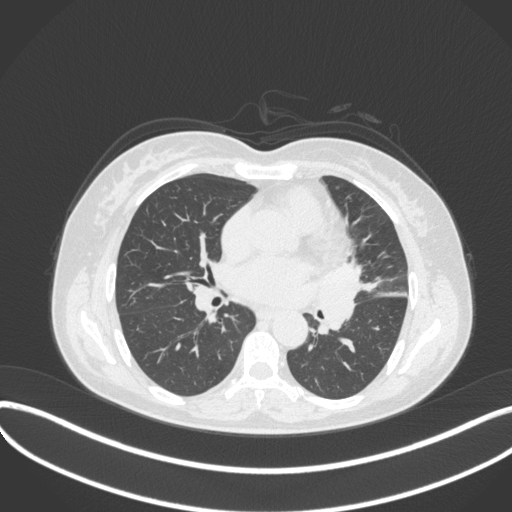
Chest CT, one axial slice. Slice 178 of 373 in the series (ordered by position). Reconstruction kernel B31f. Lung window (W 1500 / L -600 HU). 1 mm slice thickness. 512 × 512 image matrix, field of view 400 × 400 mm. Female patient, age 54 years. Case-level facts recorded for this patient, not image findings: clinical TNM (as recorded): T2a N1 M0; histopathological grade: G3.
Outlined on this slice (bounding box drawn by a radiologist):
- lung tumour (recorded histology: small cell carcinoma): bounding box (x1, y1, x2, y2) in pixels: (306, 255, 368, 334)